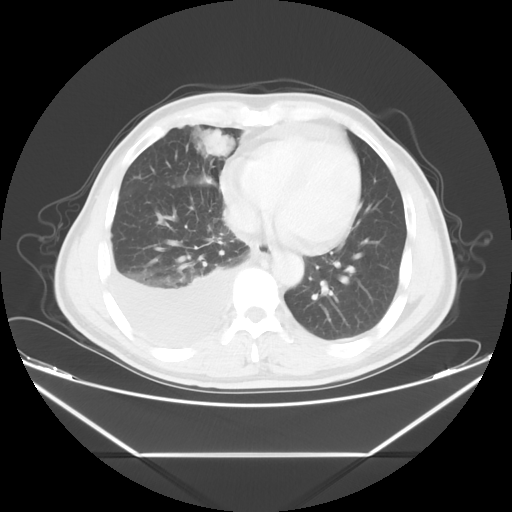
Chest CT, one axial slice. Position 18 of 56 along the scan axis. Reconstruction kernel STANDARD. 120 kVp. Lung window (W 1500 / L -600 HU). 512 × 512 image matrix. Patient: male, 57 years. From the clinical record (not read from this slice): clinical TNM (as recorded): T2 N3 M1.
Outlined on this slice (bounding box drawn by a radiologist):
- lung tumour (recorded histology: adenocarcinoma): box from (x=198, y=127) to (x=233, y=159) px